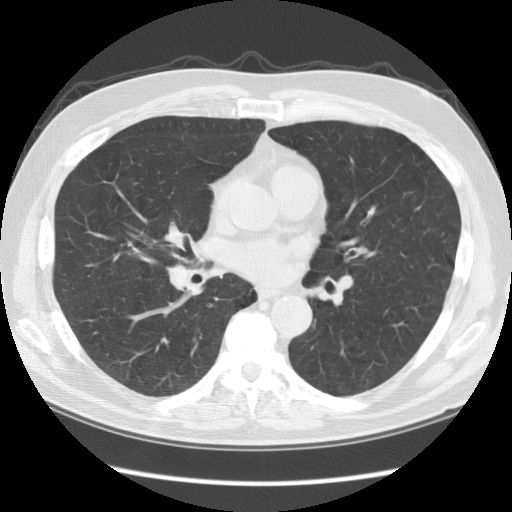
Chest CT (low-dose screening protocol), one axial image; first (baseline) screen; lung window (W 1500 / L -600 HU); 2.5 mm slice thickness; 120 kVp; 512 × 512 image matrix. Male, age 60 years at enrolment.
Expert reader's lesion annotation, bounding box <152,328,182,357> (left, top, right, bottom; pixels). Screening reader's record for this exam: no non-calcified nodule ≥4 mm recorded. Official screen result: negative screen, minor abnormalities not suspicious for lung cancer. Later outcome: lung cancer diagnosed 1051 days after this screen (after the third annual screen) — squamous cell carcinoma, clear cell type, right lower lobe, stage IV (AJCC 6th edition), 12 mm at pathology.